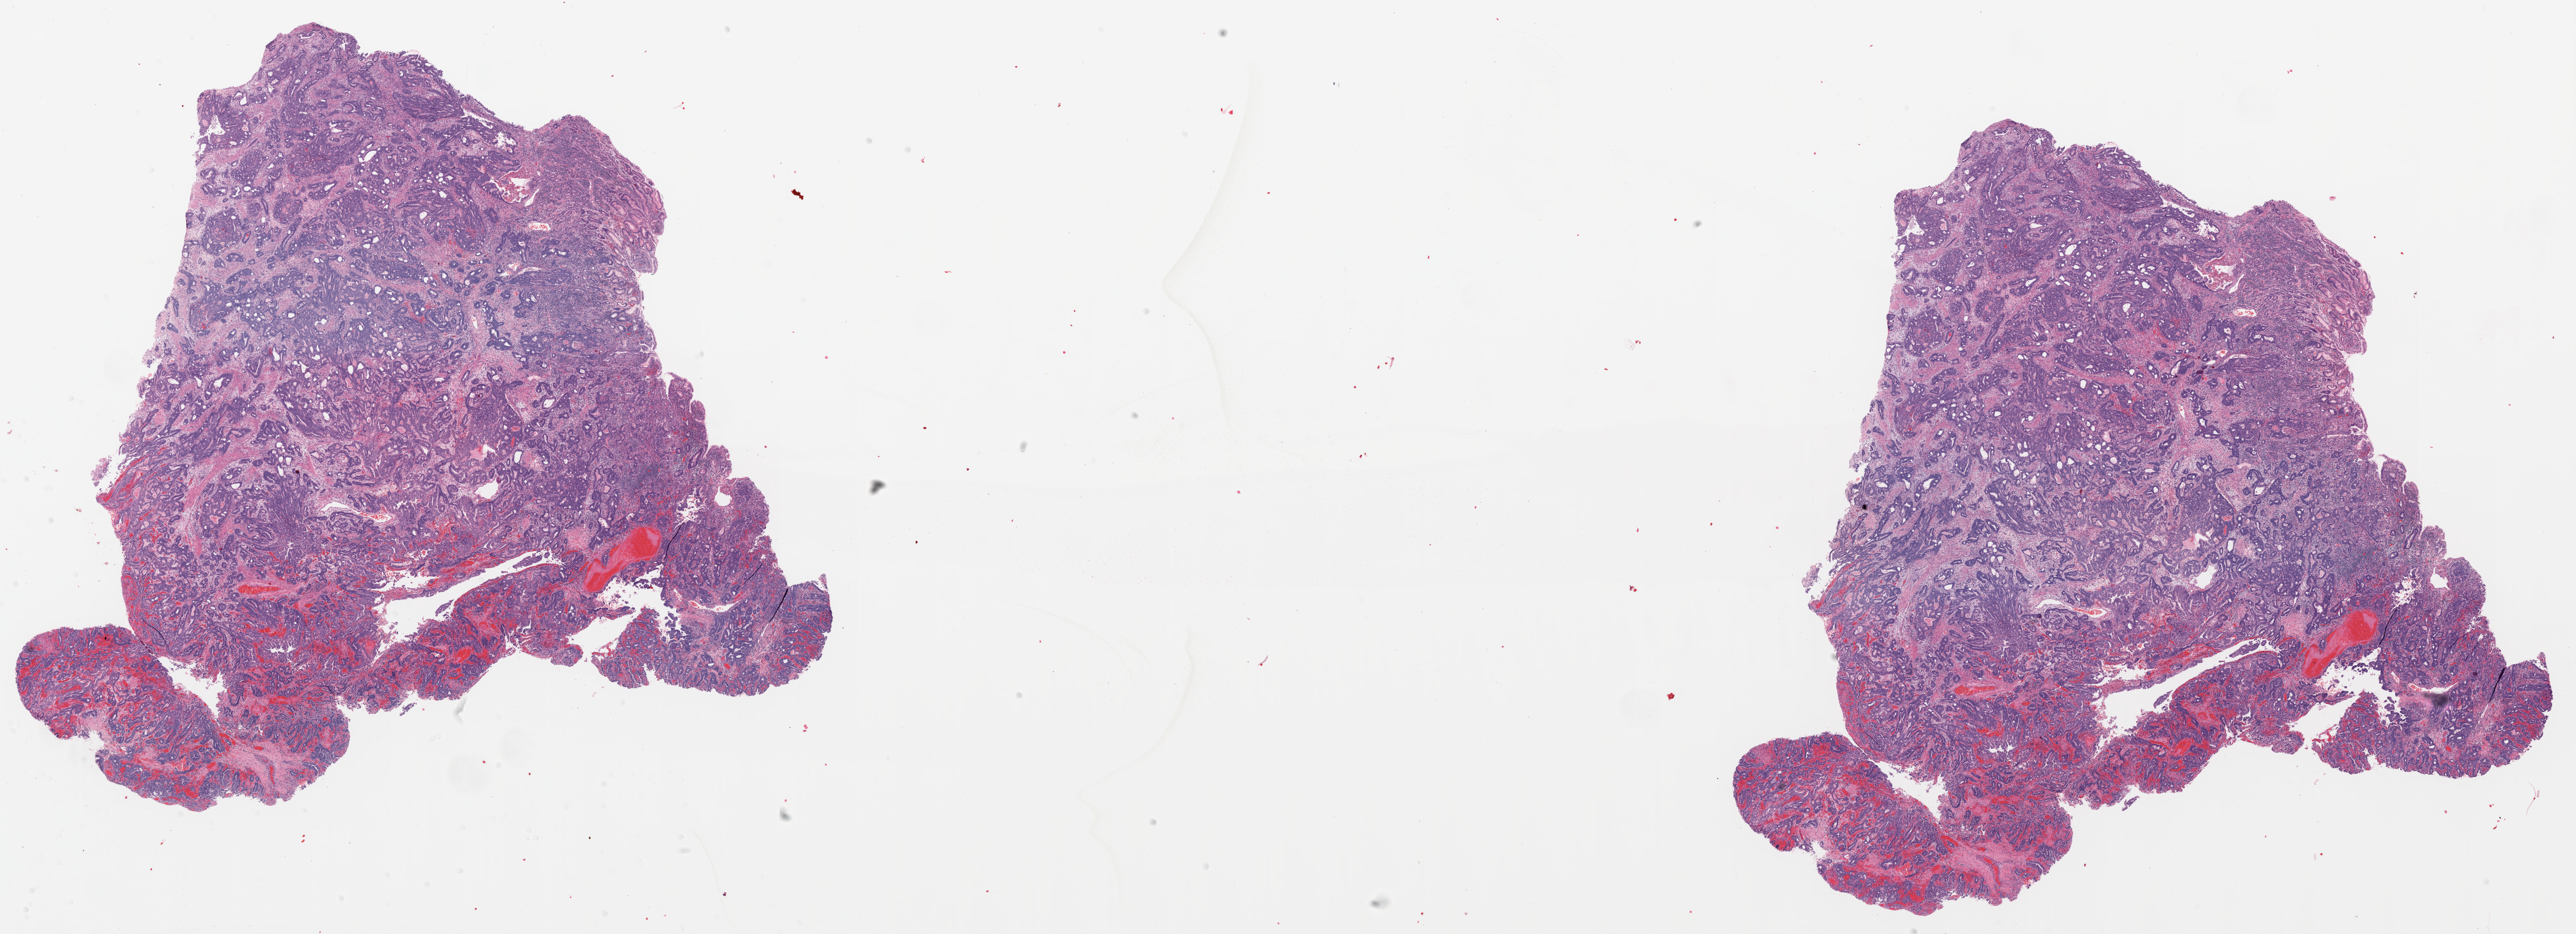
Hematoxylin and eosin (H&E) stained whole-slide image — shown as a low-resolution overview of the whole scanned area (about 33.0 x 12.0 mm, from a 20x scan), formalin-fixed paraffin-embedded (FFPE) diagnostic section, primary tumour sample from the stomach. Patient sex: male. Histologic grade: G2 (moderately differentiated).
* diagnosis: Adenocarcinoma, NOS (cardia, NOS)
* TNM: T3 N1 M0
* AJCC pathologic stage: IIIA (6th edition)
* lymph nodes positive (case pathology): 2 of 12 examined